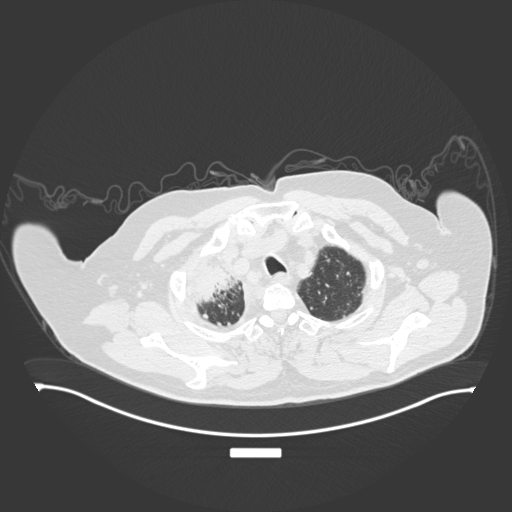
Chest CT, one axial slice. Slice 170 of 201 in the series (ordered by position). Reconstruction kernel B30f. 120 kVp. Lung window (W 1500 / L -600 HU). 512 × 512 image matrix. Male patient, age 69 years. From the clinical record (not read from this slice): clinical TNM (as recorded): T4 N3 M1.
Annotated regions visible in this slice (rectangle marked by the reading radiologist):
- lung tumour (recorded histology: adenocarcinoma): bounding box [x1, y1, x2, y2] px = [188, 256, 247, 311]